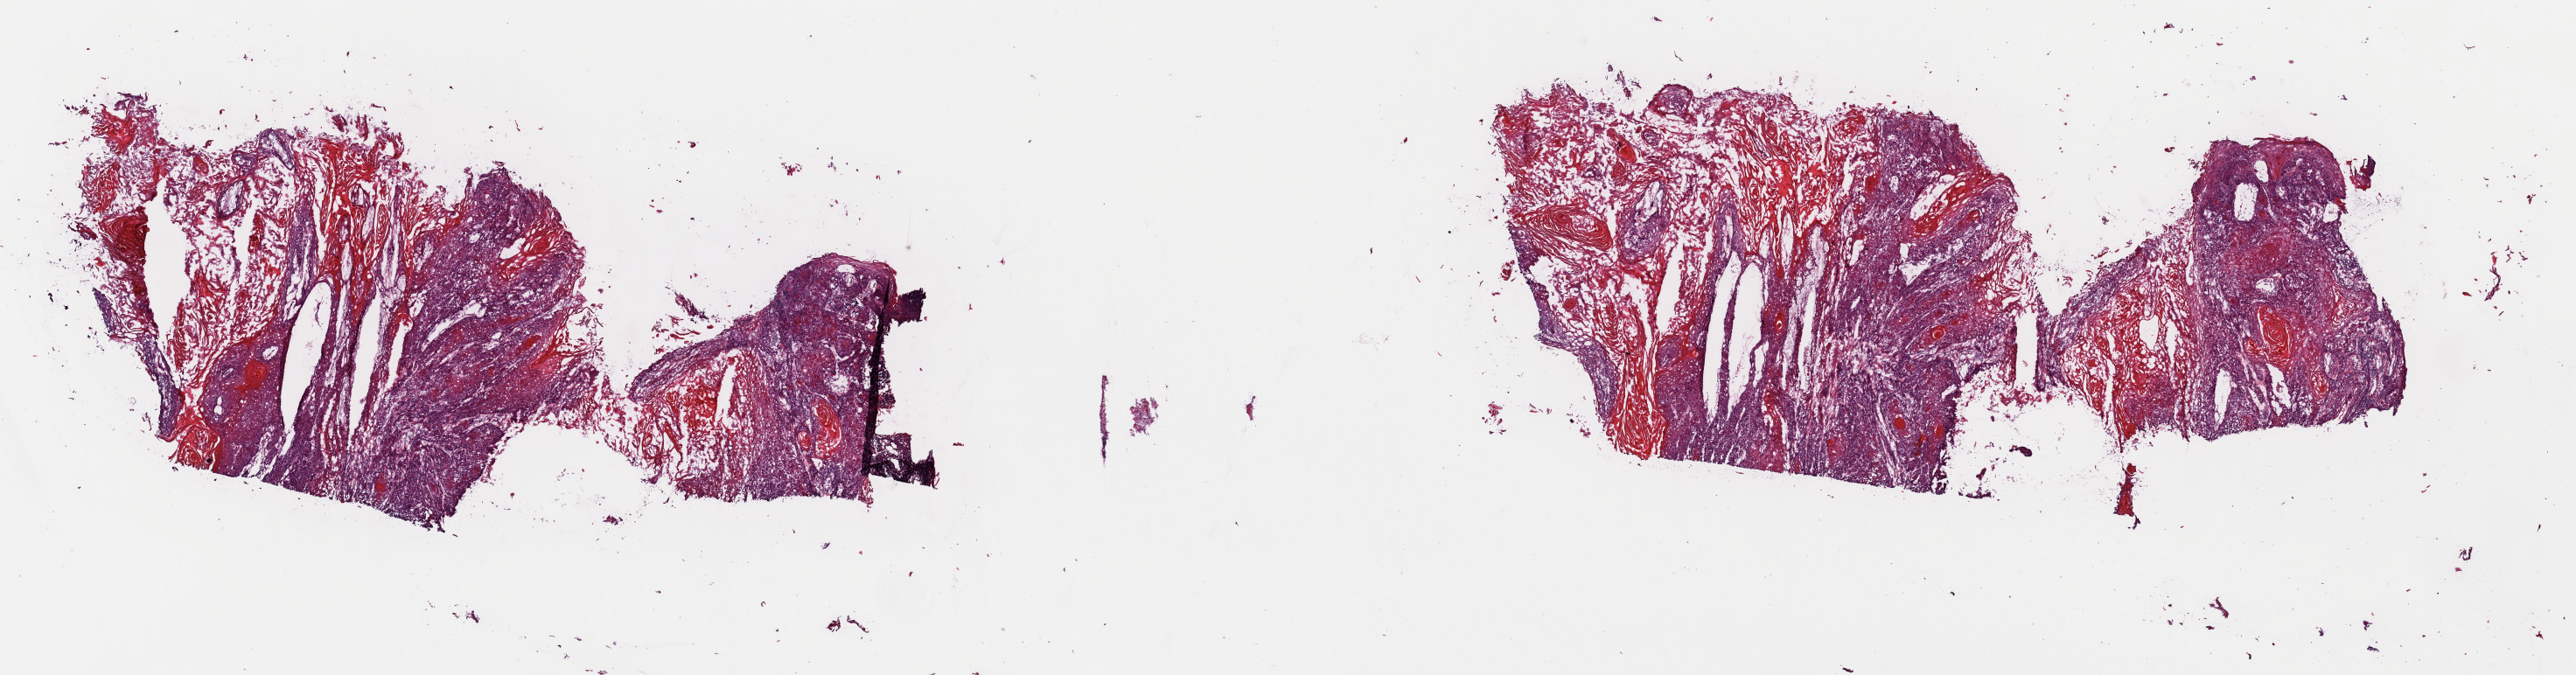
Digitized H&E tissue section (whole slide) — whole scanned area (about 23.3 x 6.1 mm) shown as a low-resolution overview, frozen section, primary tumour sample from the head and neck. Patient: female, age at initial diagnosis 72 years. Histologic grade: G1 (well differentiated). Composition of this section per pathologist review: tumour cells 94%, tumour nuclei 100%, normal cells 0%, stromal cells 5%, necrosis 1%. Inflammatory infiltration, as recorded: lymphocyte infiltration 1%, monocyte infiltration 1%, neutrophil infiltration 1%.
• lymph nodes positive (case pathology): 1 of 2 examined
• AJCC pathologic stage: III (7th edition)
• TNM: T2 N1 M0
• laterality: midline
• diagnosis: Squamous cell carcinoma, NOS (tongue, NOS)